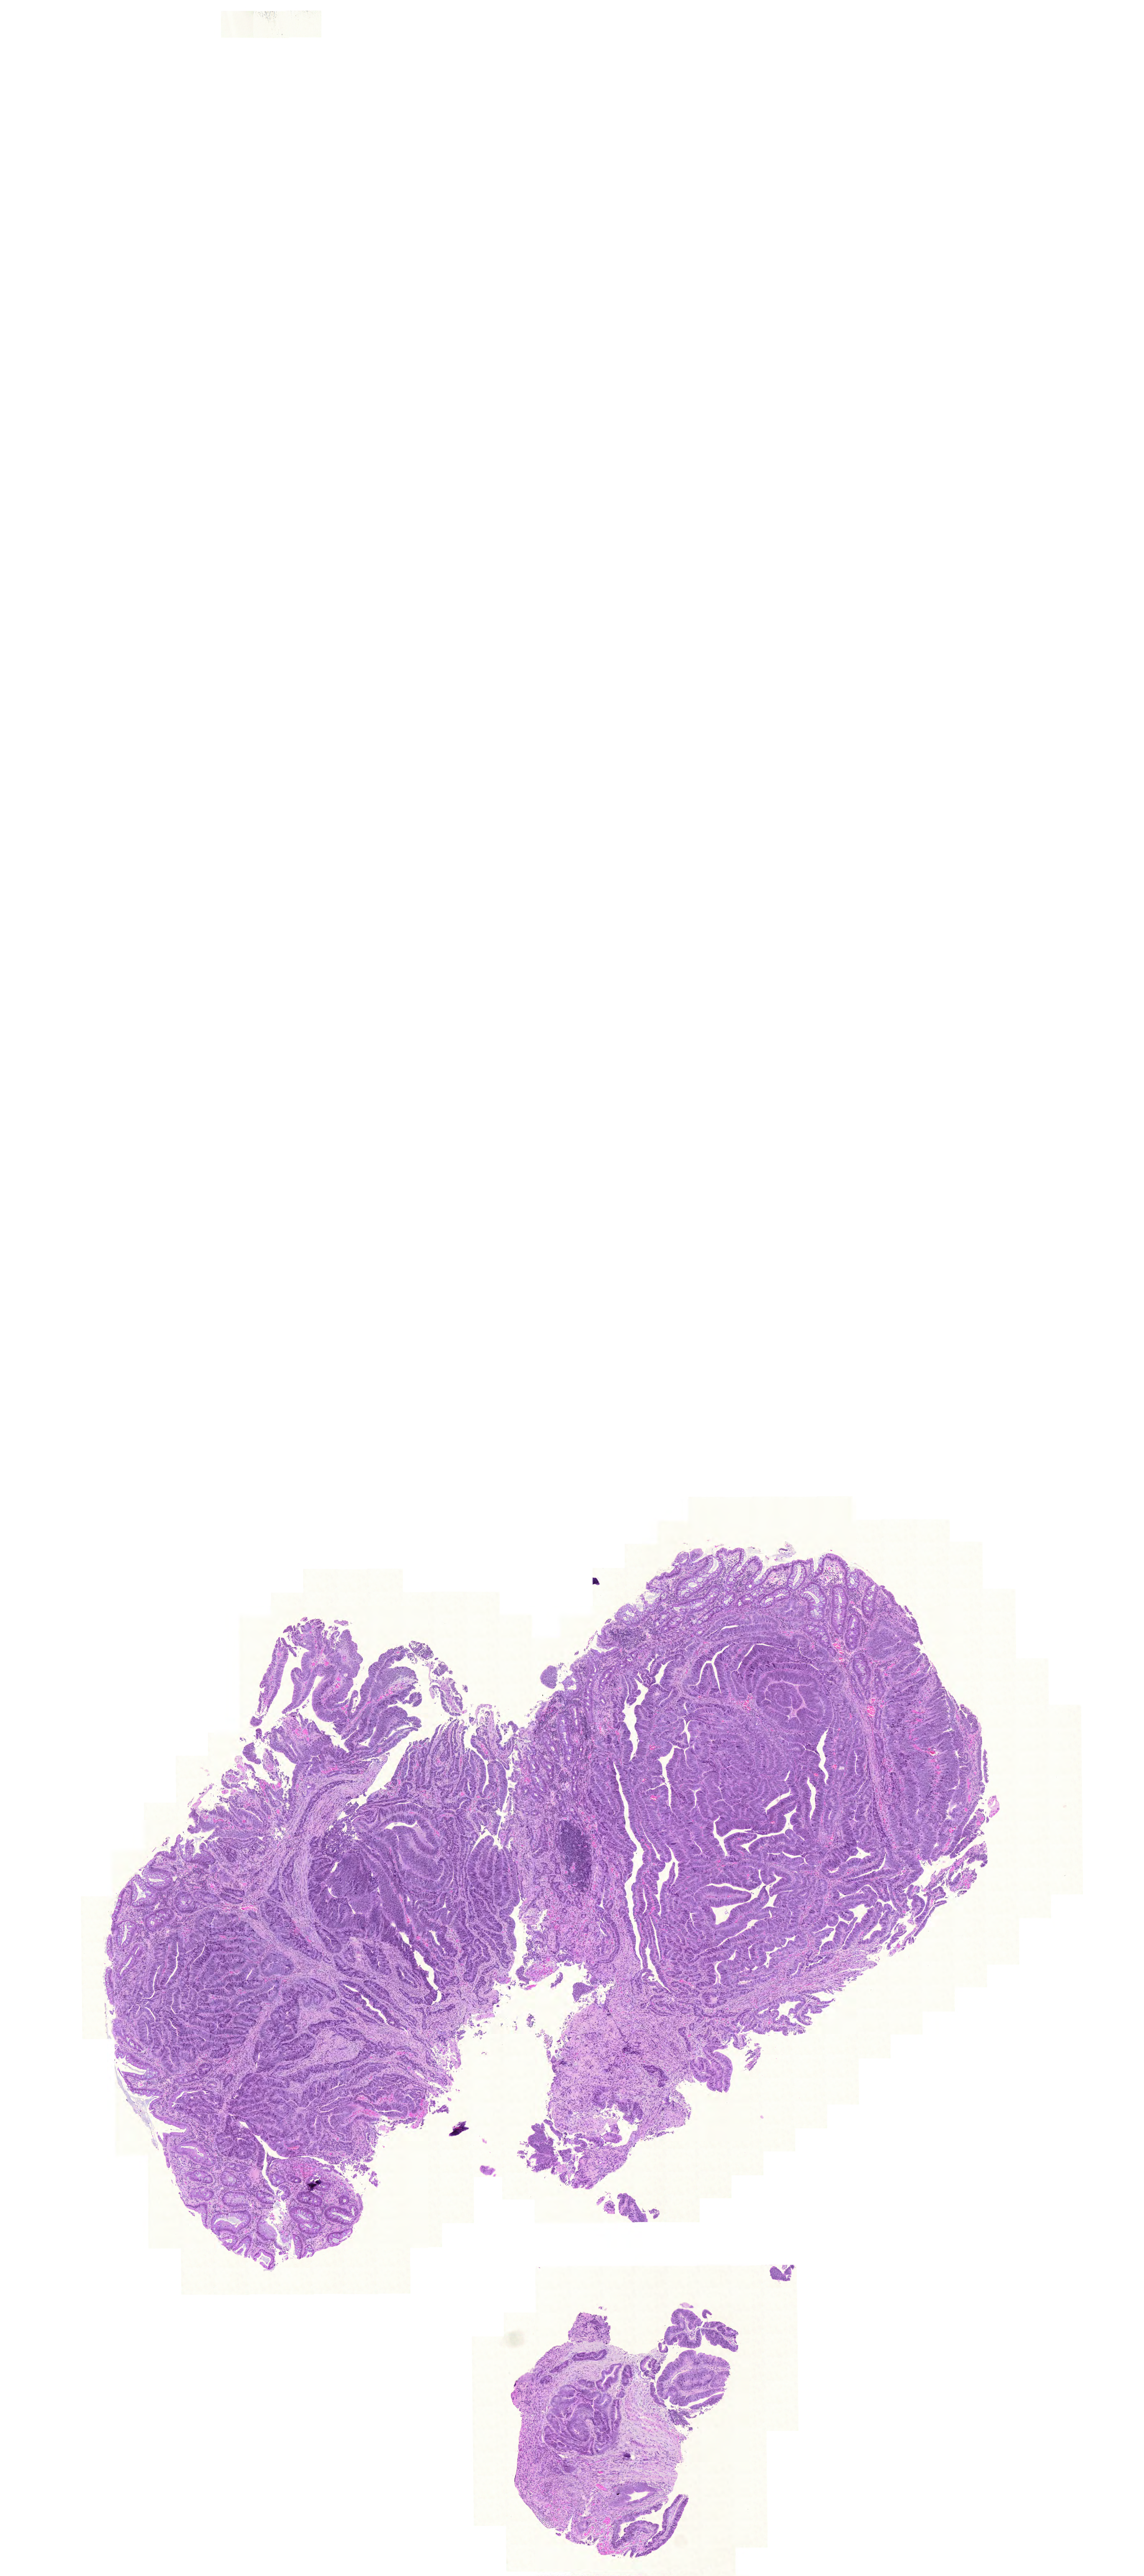
Hematoxylin and eosin (H&E) stained whole-slide image — low-resolution overview of the scanned area, about 10.2 x 22.9 mm (acquisition: 20x scan). FFPE section. Primary tumour sample from the colon. Patient: female, age at initial diagnosis 41 years.
AJCC pathologic stage: IIA (6th edition). Histologic diagnosis: Adenocarcinoma, NOS.